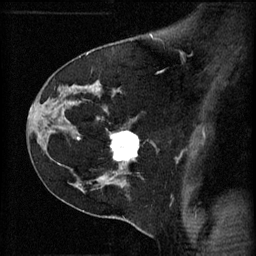
Breast MRI (dynamic contrast-enhanced), one sagittal slice. 3 images stored at this slice position (order not interpretable as contrast timing). 1.5 T. TE 4.2 ms, TR 11 ms. 2 mm slice thickness. 256 × 256 image matrix, field of view 180 × 180 mm. Female patient, age 45 years.
Outlined on this slice (semi-automatic segmentation, software-assisted and operator-edited):
- analysis volume of interest (the breast-tissue region the enhancement analysis was run in; not a lesion): bounding box (x1, y1, x2, y2) in pixels: (112, 132, 141, 171)
- tumour enhancement mask (voxels above the 70 % enhancement threshold inside the analysis volume of interest): (112, 132, 139, 169)